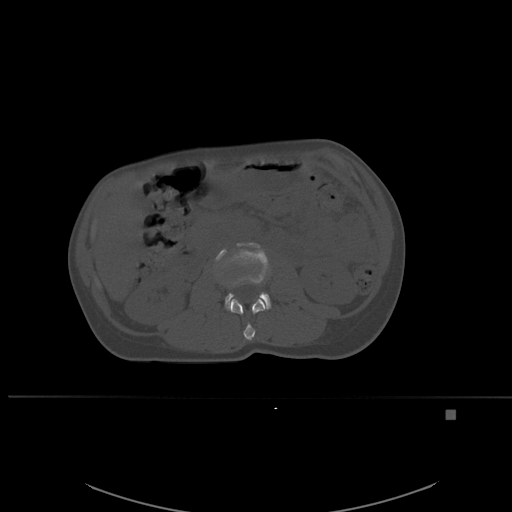
CT including the spine, one axial slice; bone window (W 1800 / L 400 HU); 1.5 mm slice thickness; 512 × 512 image matrix. Female patient, age 45 years. From the clinical record (not read from this slice): primary cancer: lung.
Annotated regions visible in this slice (semi-automatic segmentation, software-assisted and operator-edited):
- L2 vertebra: bounding box <230,298,266,341> (left, top, right, bottom; pixels)
- L3 vertebra: <215,242,271,310>